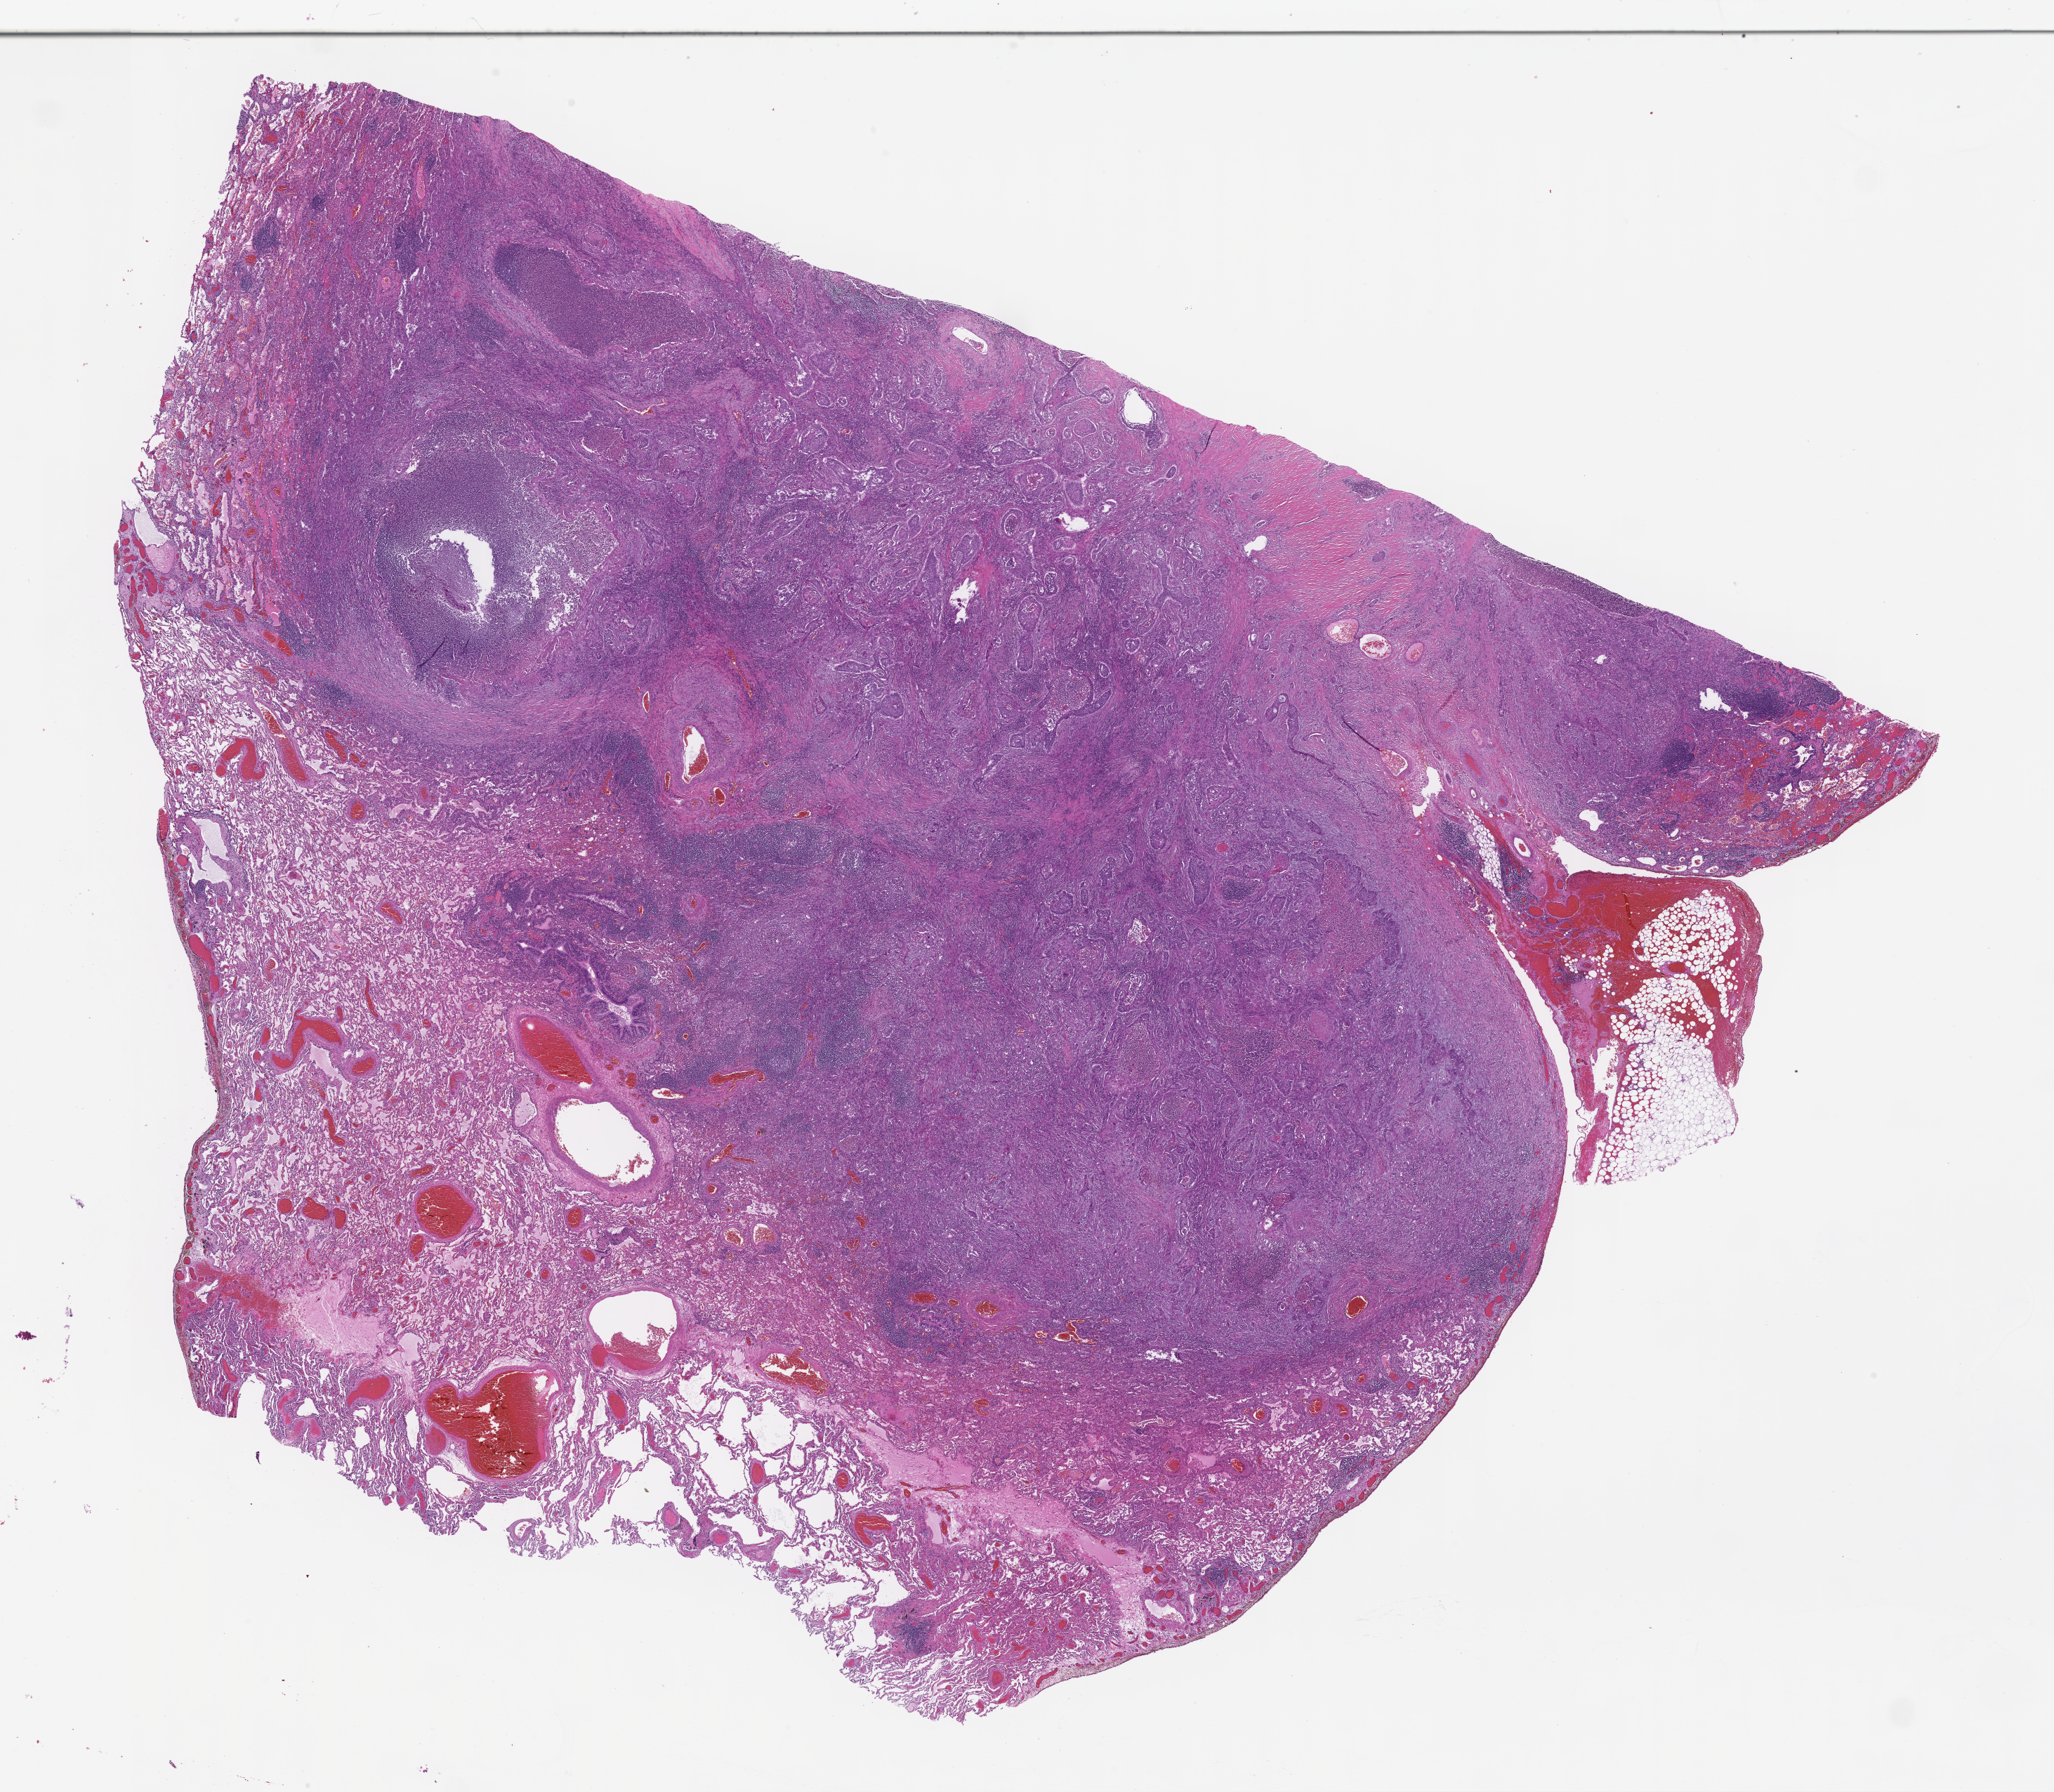
Haematoxylin and eosin whole-slide image — shown as a low-resolution overview of the whole scanned area (about 23.6 x 20.6 mm), FFPE section, tissue site: lung. Female patient.
* this section: primary tumor
* diagnosis: Non-Small Cell Lung Carcinoma